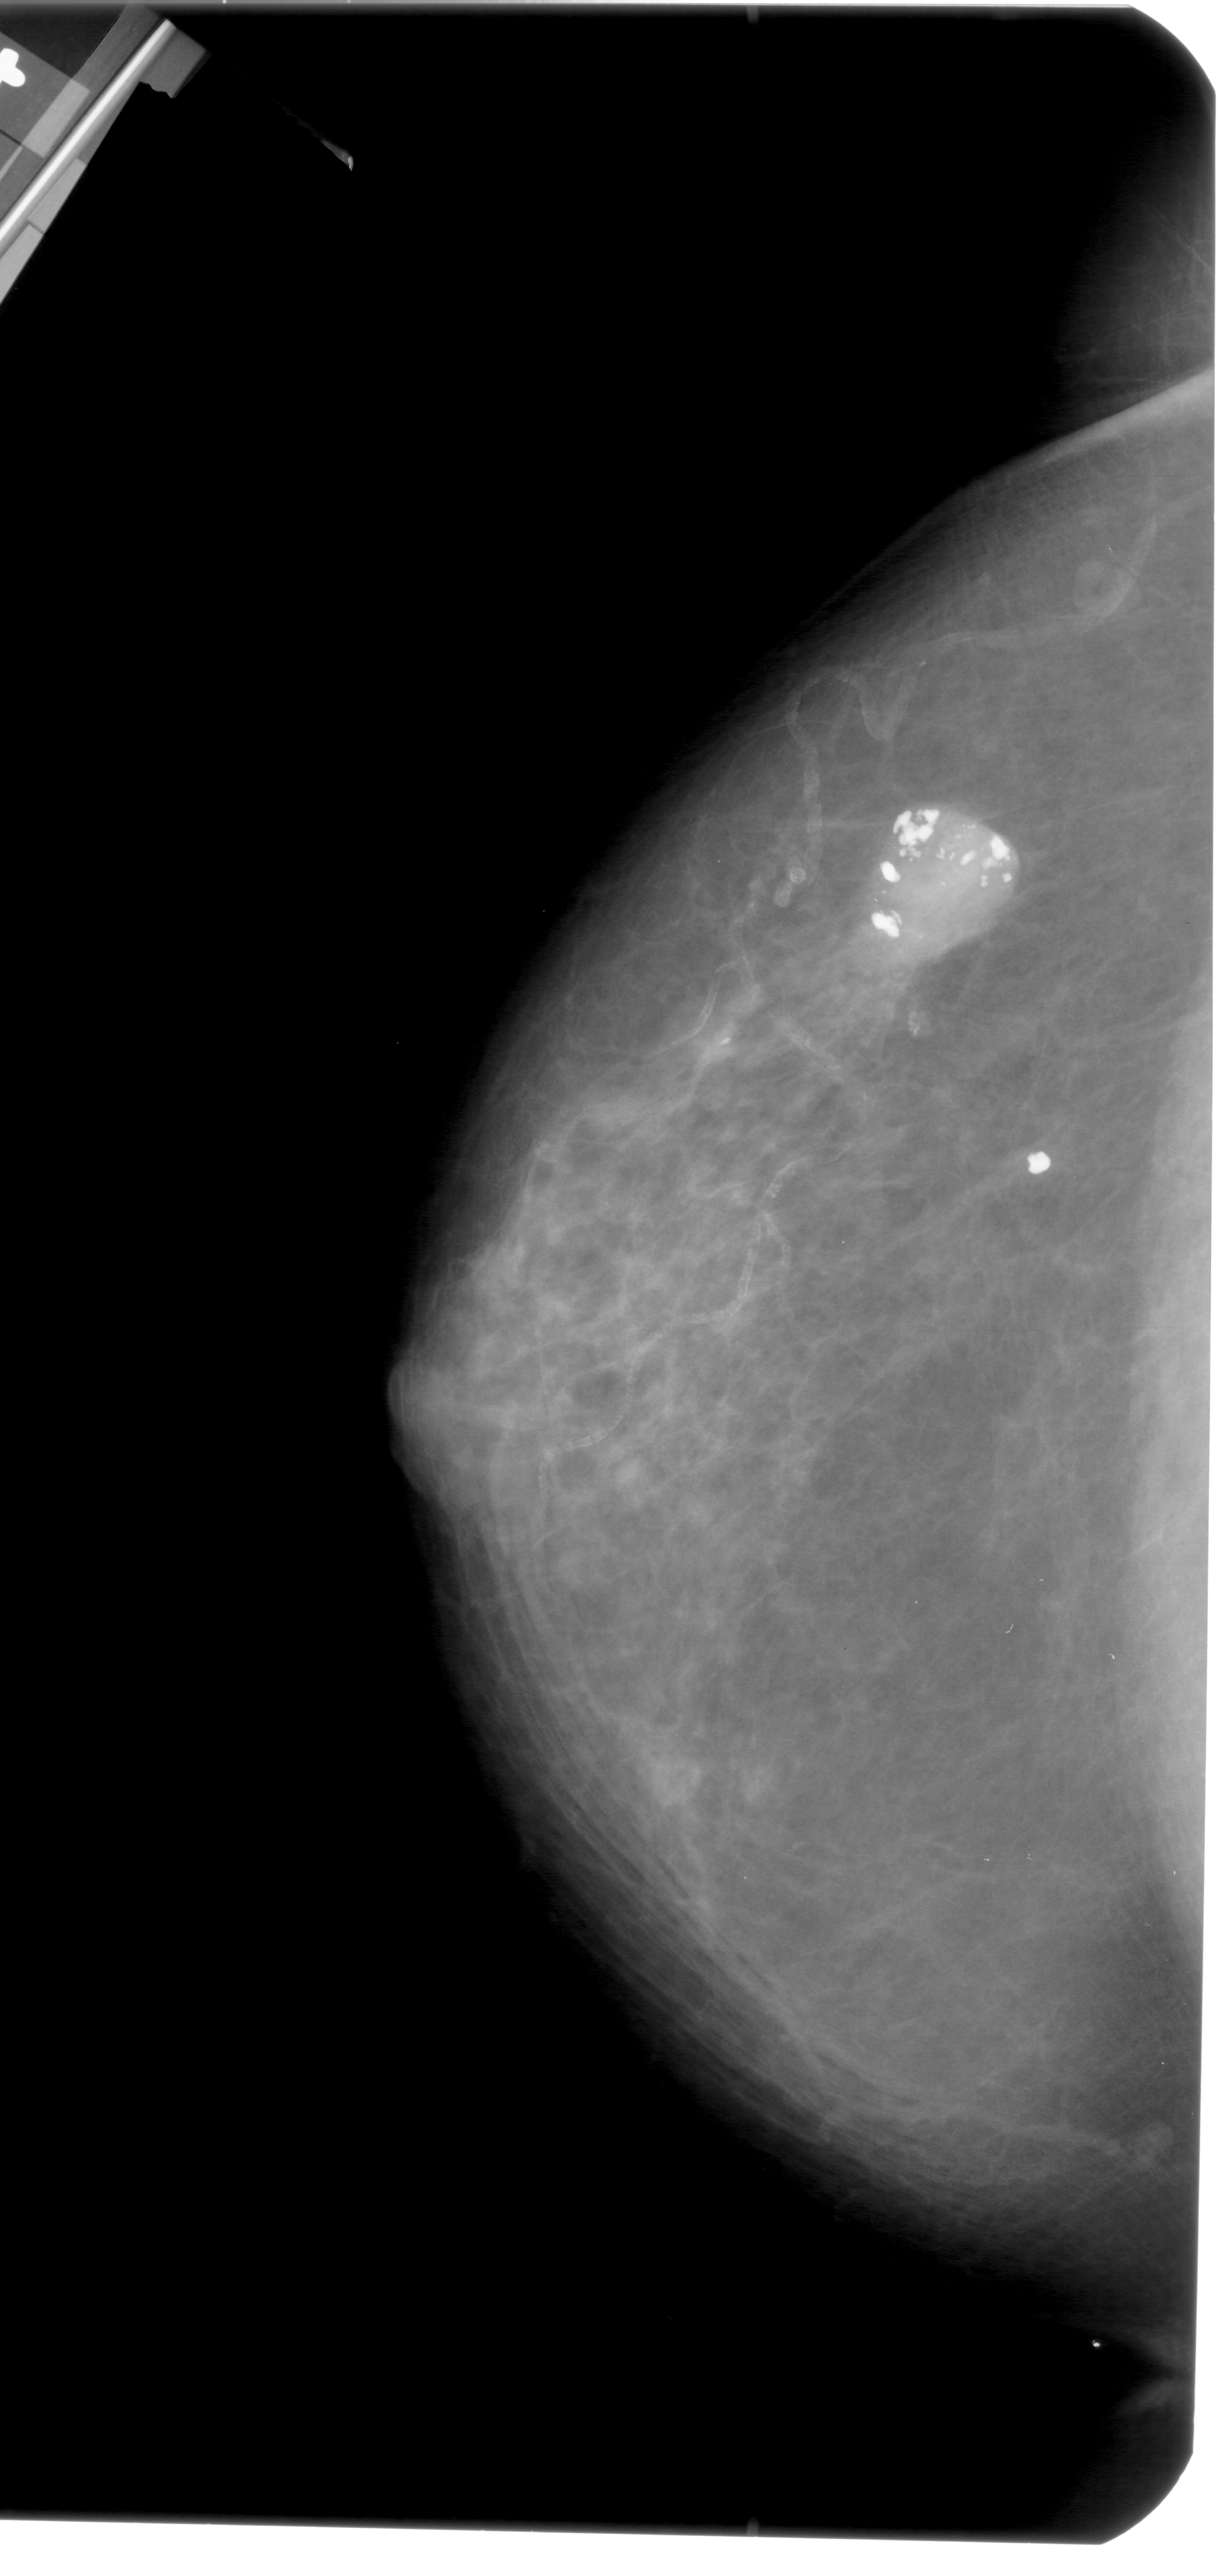
Mammogram (digitized film); left breast; CC view; breast composition: heterogeneously dense (BI-RADS density category 3 of 4).
- Marked abnormality: calcifications, morphology amorphous; BI-RADS assessment category 2; pathology (as recorded): benign.